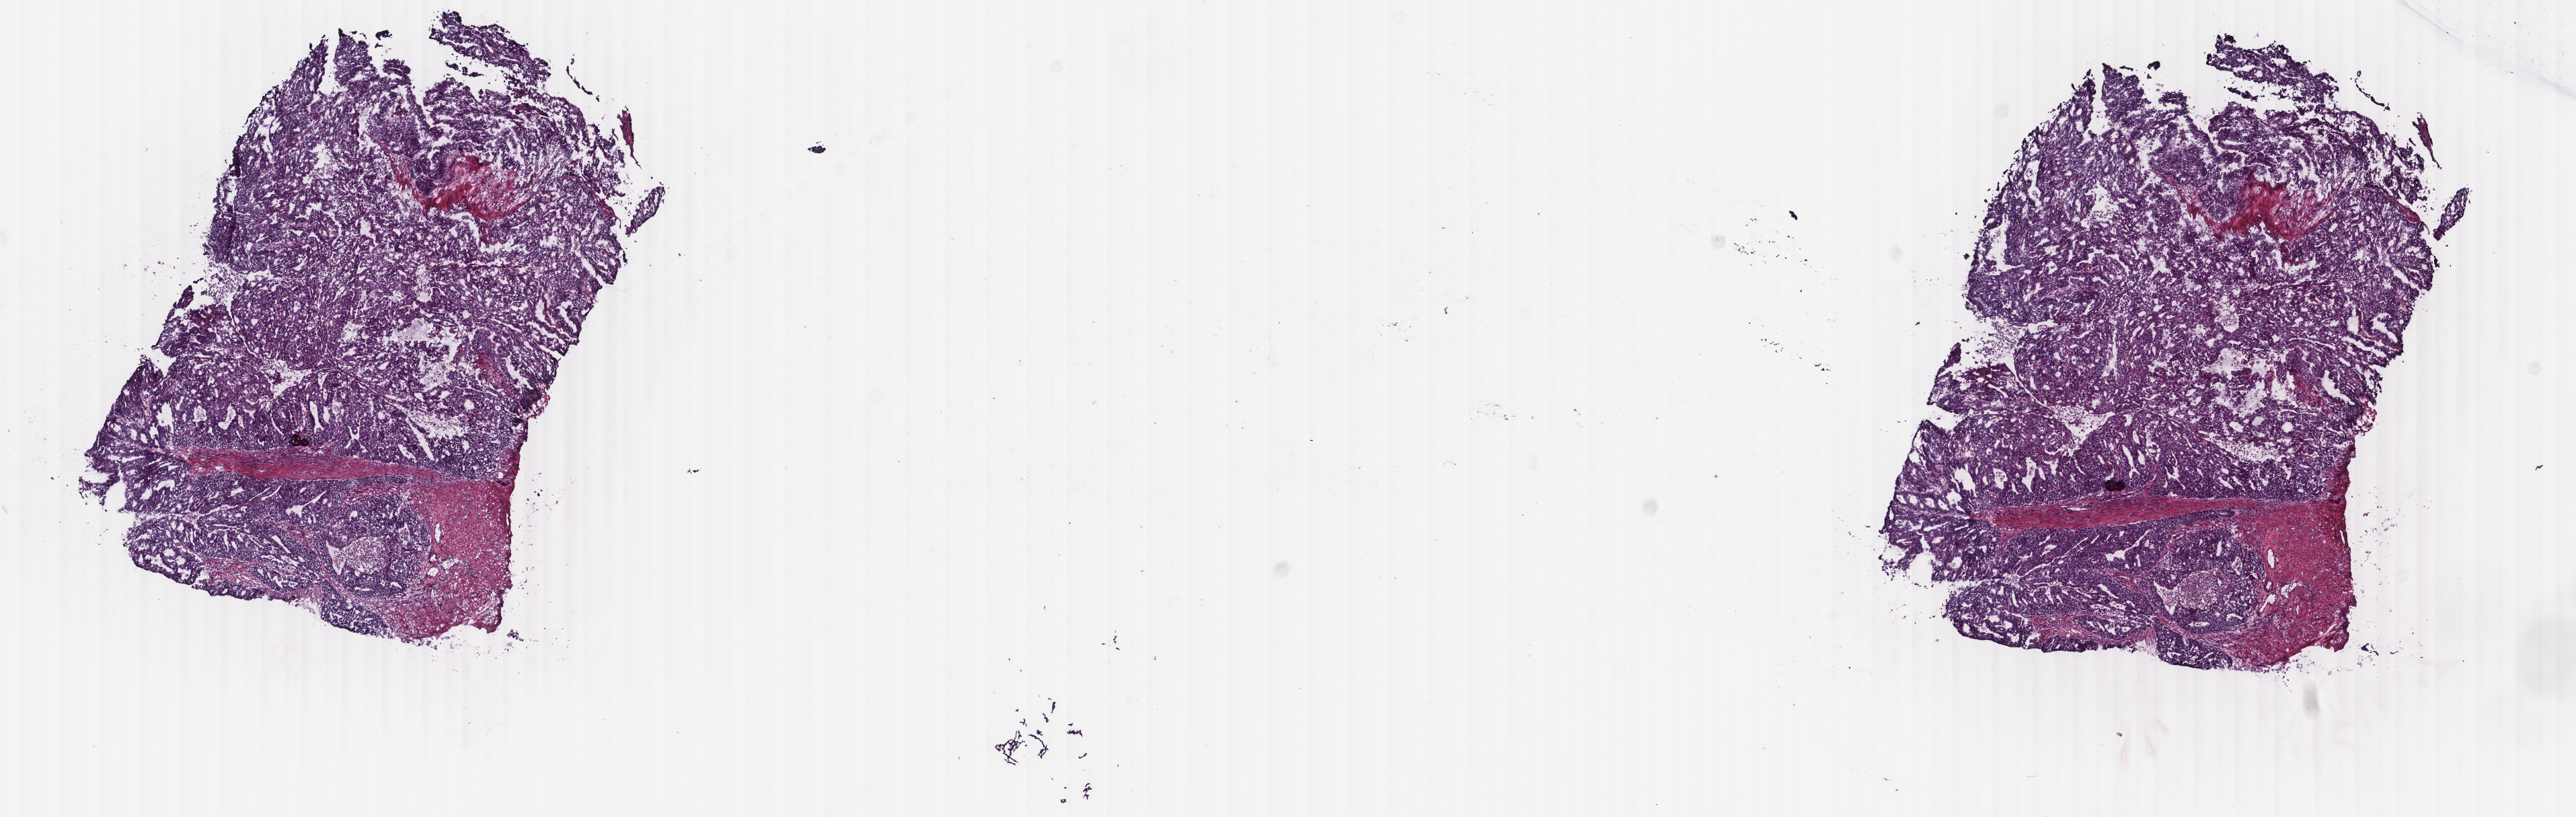
Digitized H&E-stained tissue section (whole slide), whole scanned area (about 15.2 x 4.8 mm) shown as a low-resolution overview; frozen section from the top of the tissue portion; sample: primary tumour, uterus. Female, age 68 years at initial diagnosis.
Pathologic diagnosis: Endometrioid adenocarcinoma, NOS (endometrium).